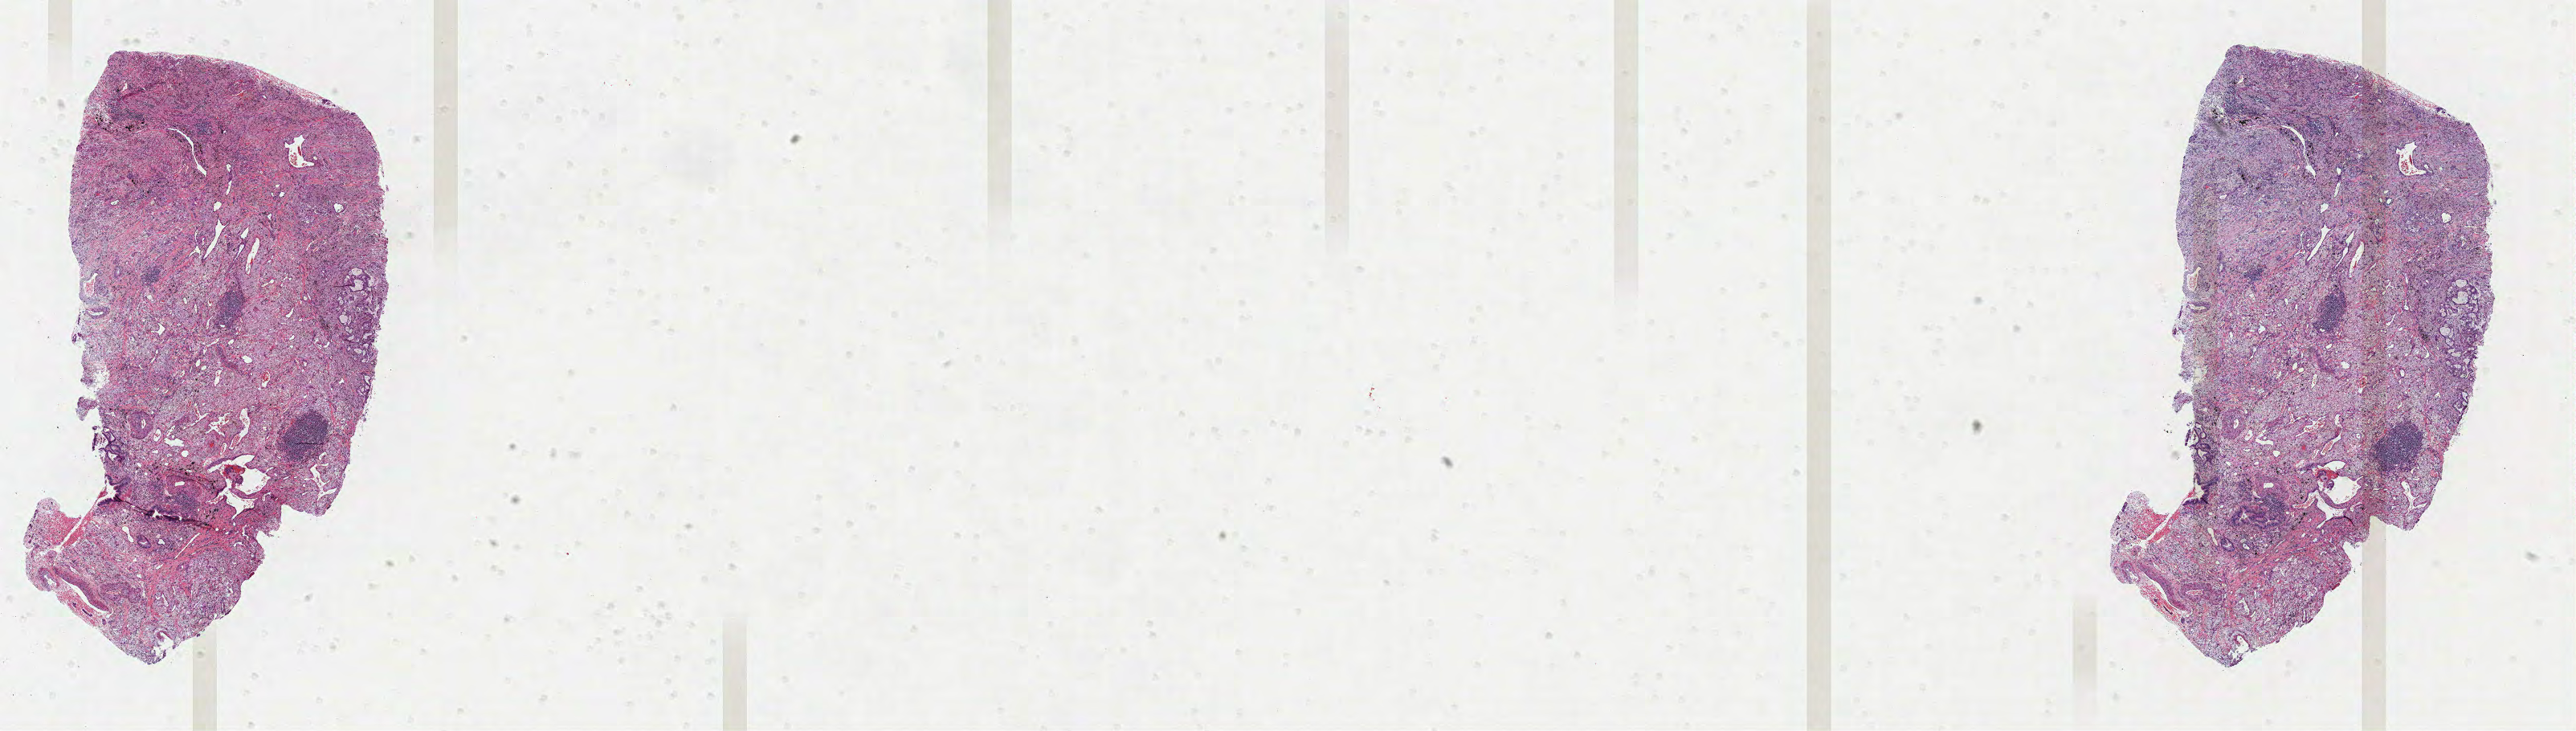
H&E-stained whole-slide image, low-resolution overview of the scanned area, about 25.9 x 7.3 mm (slide scanned at 40x); FFPE section; sample: primary tumour, lung. Male patient; age at initial diagnosis 64 years.
Diagnosis: Adenocarcinoma with mixed subtypes (middle lobe, lung). AJCC pathologic stage: IB.